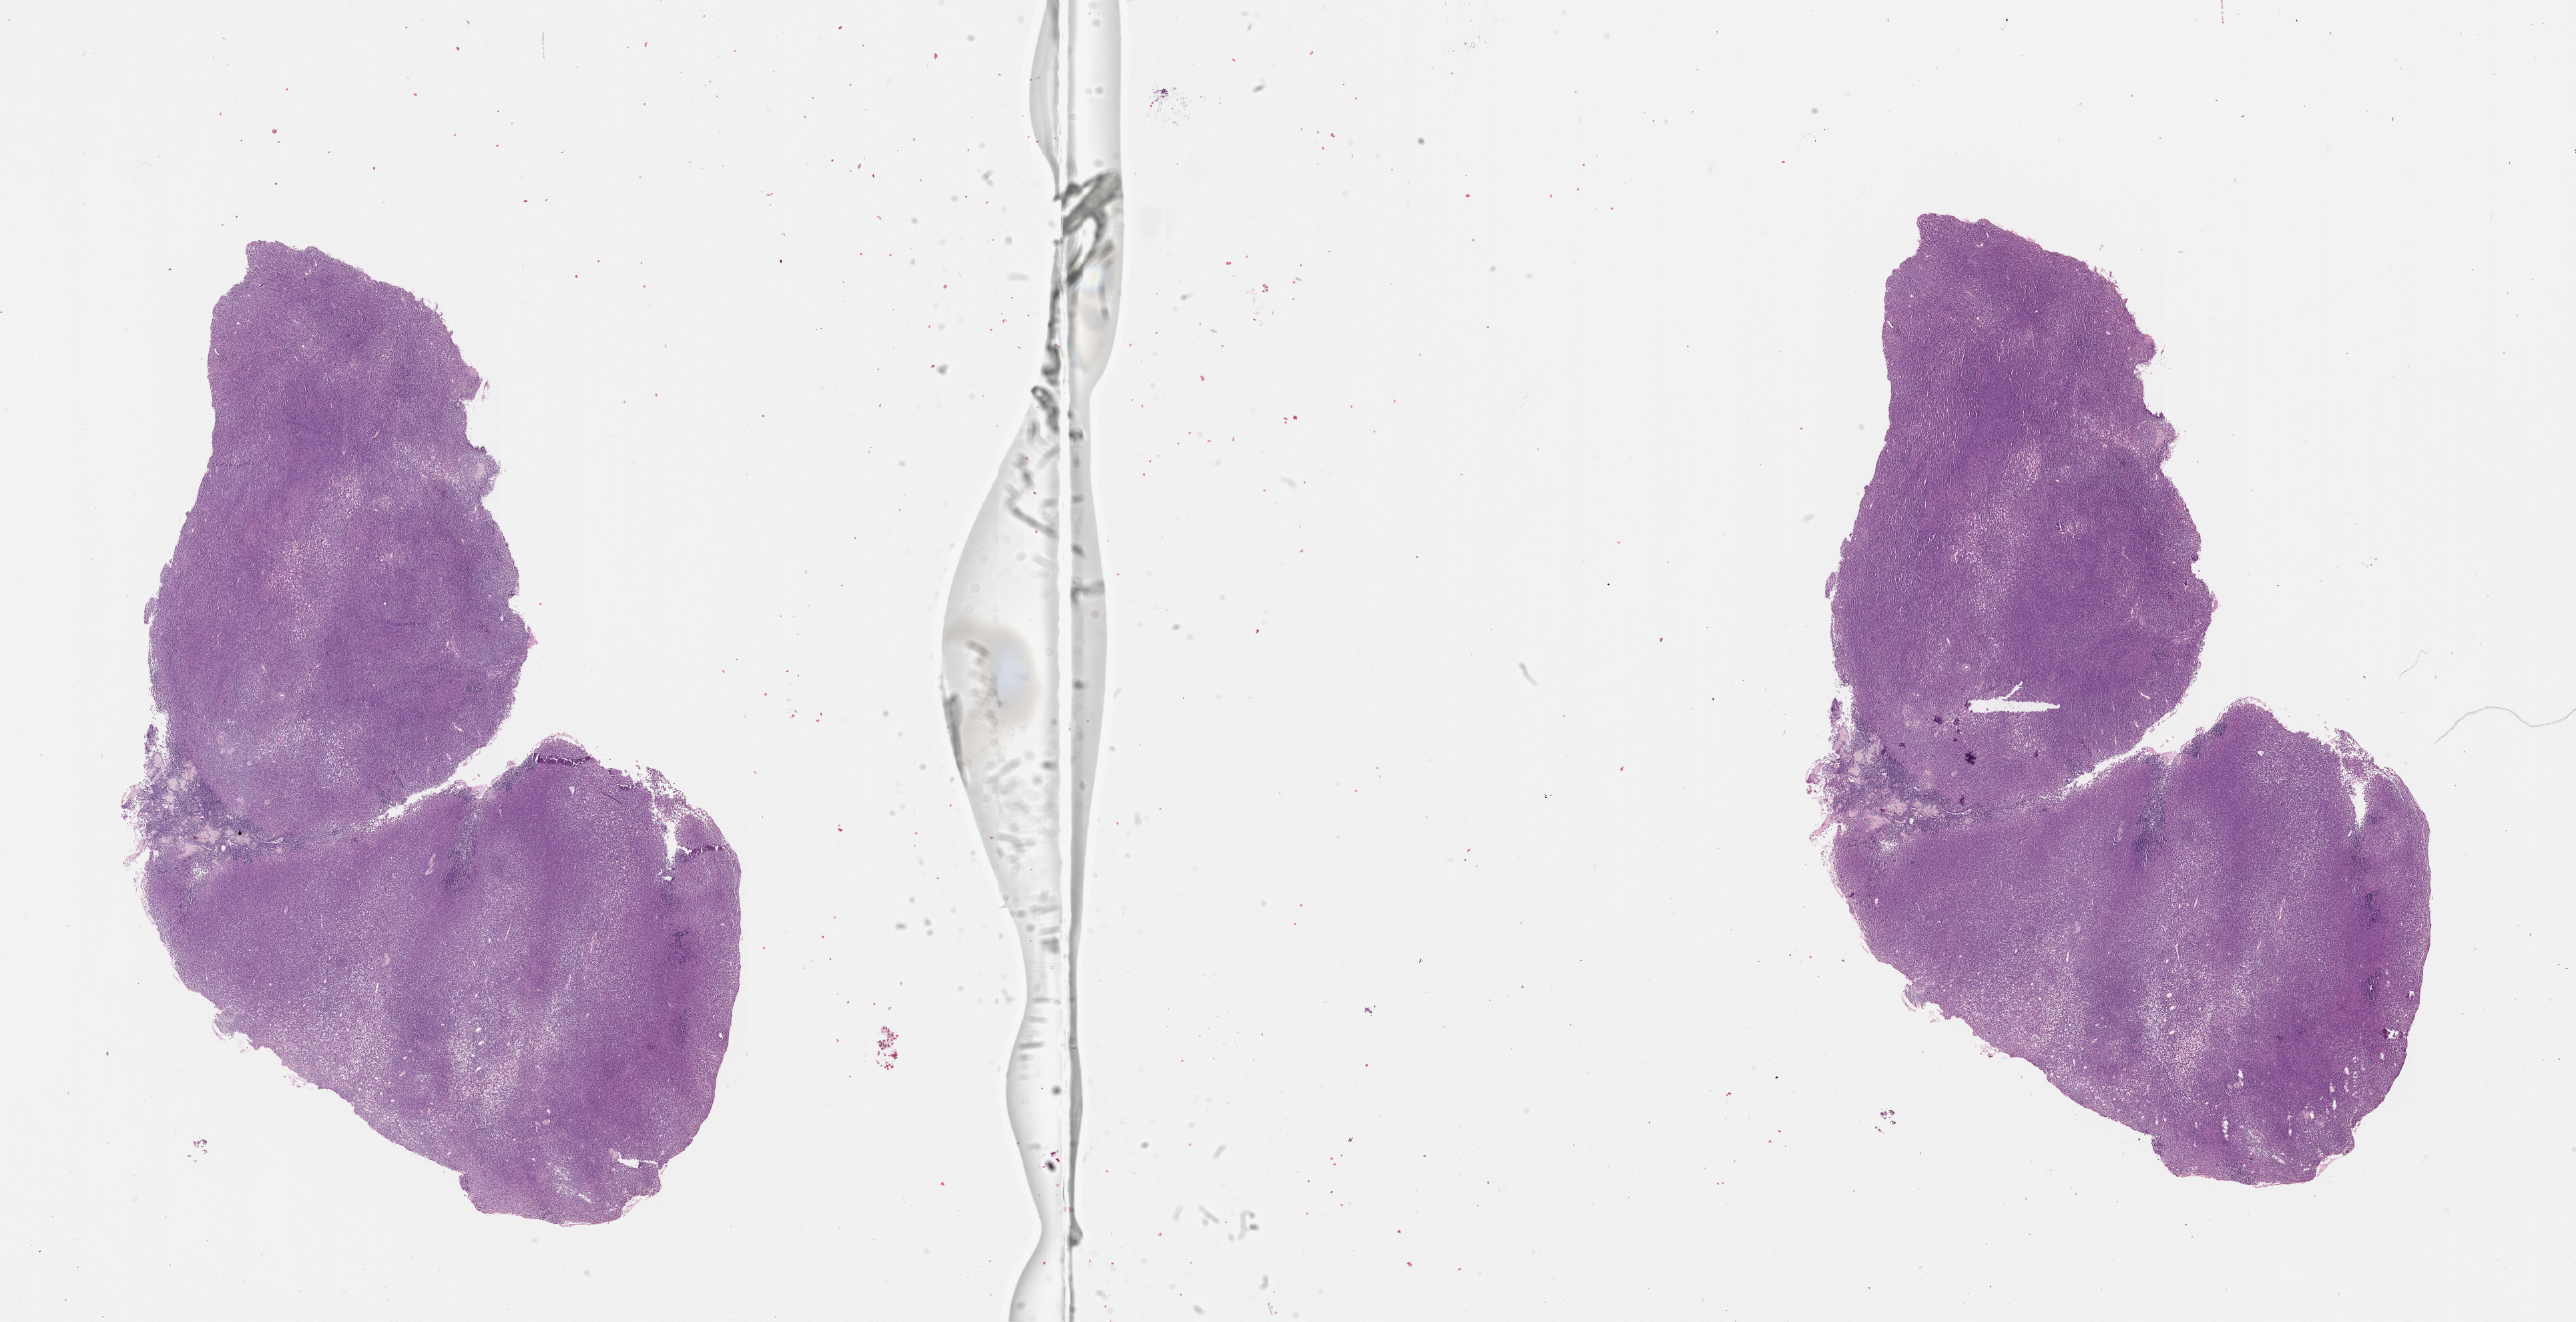
Digitized H&E tissue section (whole slide) — low-resolution overview of the scanned area, about 31.1 x 15.9 mm (acquisition: 20x scan), tumour tissue sample, sampled site: skin. 80-year-old female patient.
This section: metastatic tumour tissue. Patient diagnosis: Malignant melanoma, NOS.